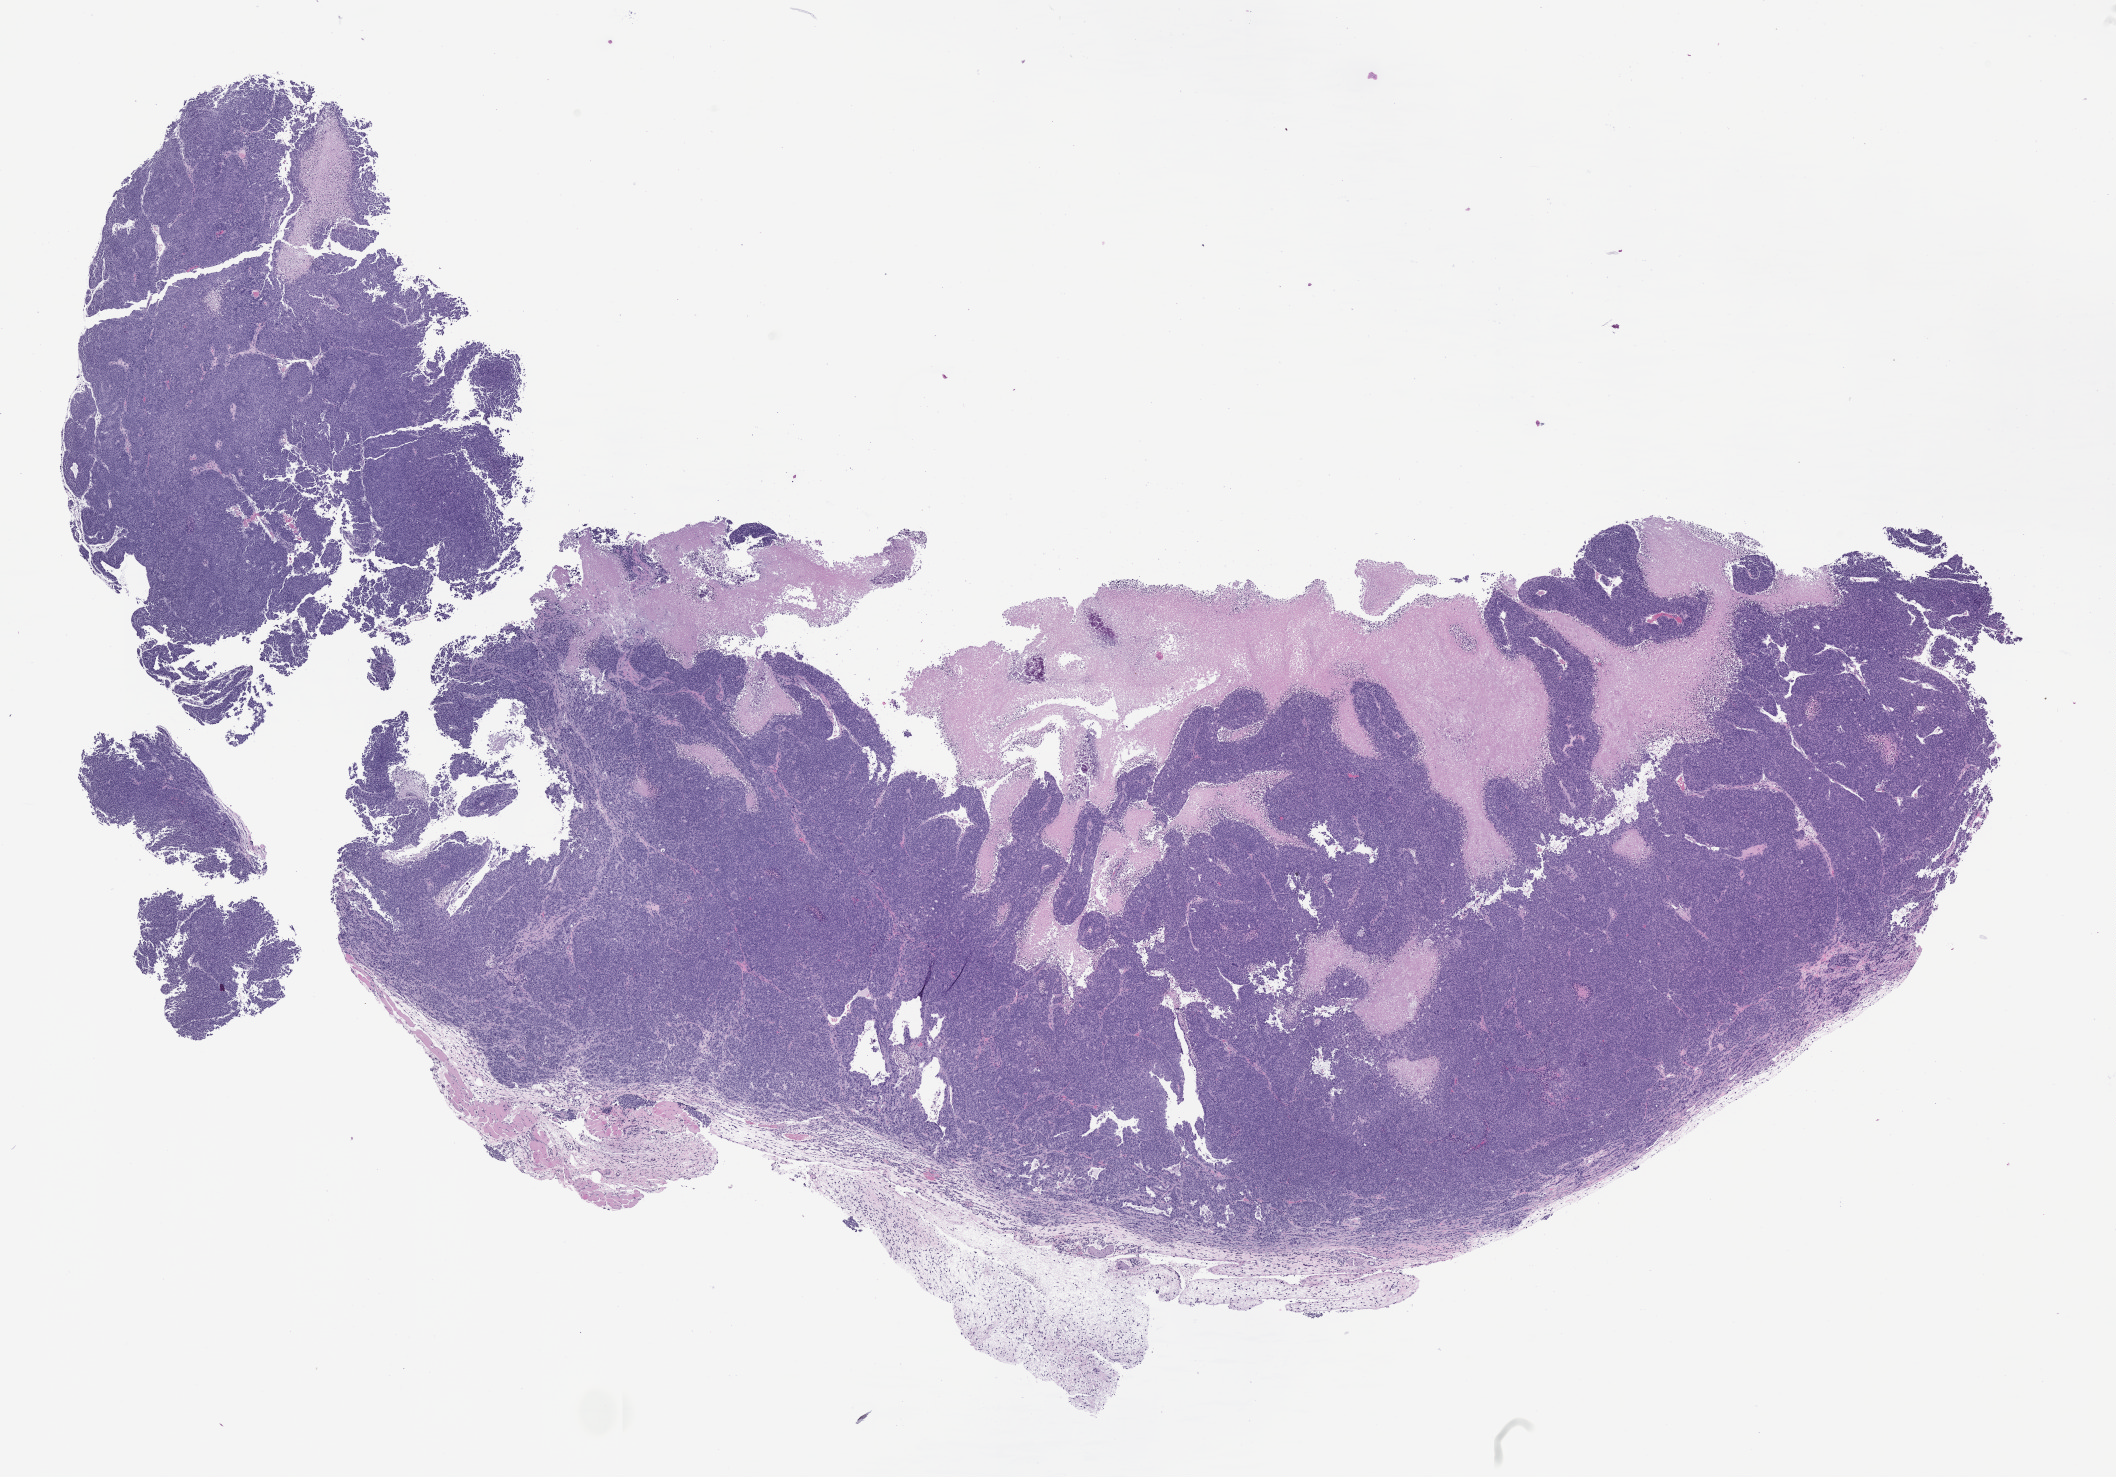
H&E whole-slide image of a patient-derived xenograft (PDX) tumor grown in a mouse, passage 2, whole scanned area (about 17.0 x 11.9 mm) shown as a low-resolution overview. Formalin-fixed, paraffin-embedded (FFPE) tissue. Originating tumor site category: cervix.
Originating patient diagnosis: Cervical Adenocarcinoma.